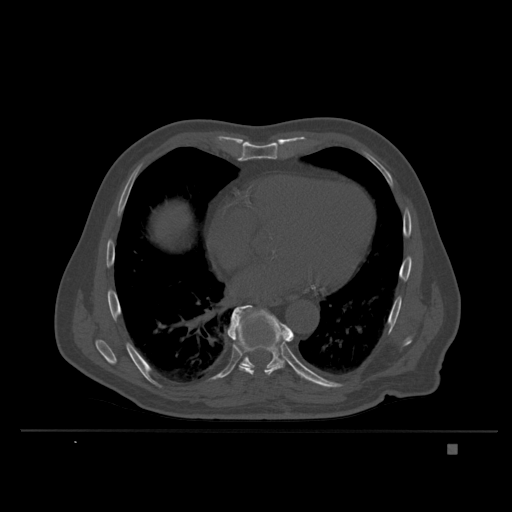
CT including the spine, one axial slice; position 222 of 435 along the scan axis; bone window (W 1800 / L 400 HU); 1.5 mm slice thickness; 512 × 512 image matrix. Male patient, age 73 years. From the clinical record (not read from this slice): primary cancer: skin.
Outlined on this slice (semi-automatically segmented with operator editing):
- T6 vertebra: bounding box <235,338,288,354> (left, top, right, bottom; pixels)
- T8 vertebra: <228,315,294,376>
- T9 vertebra: <228,305,307,380>